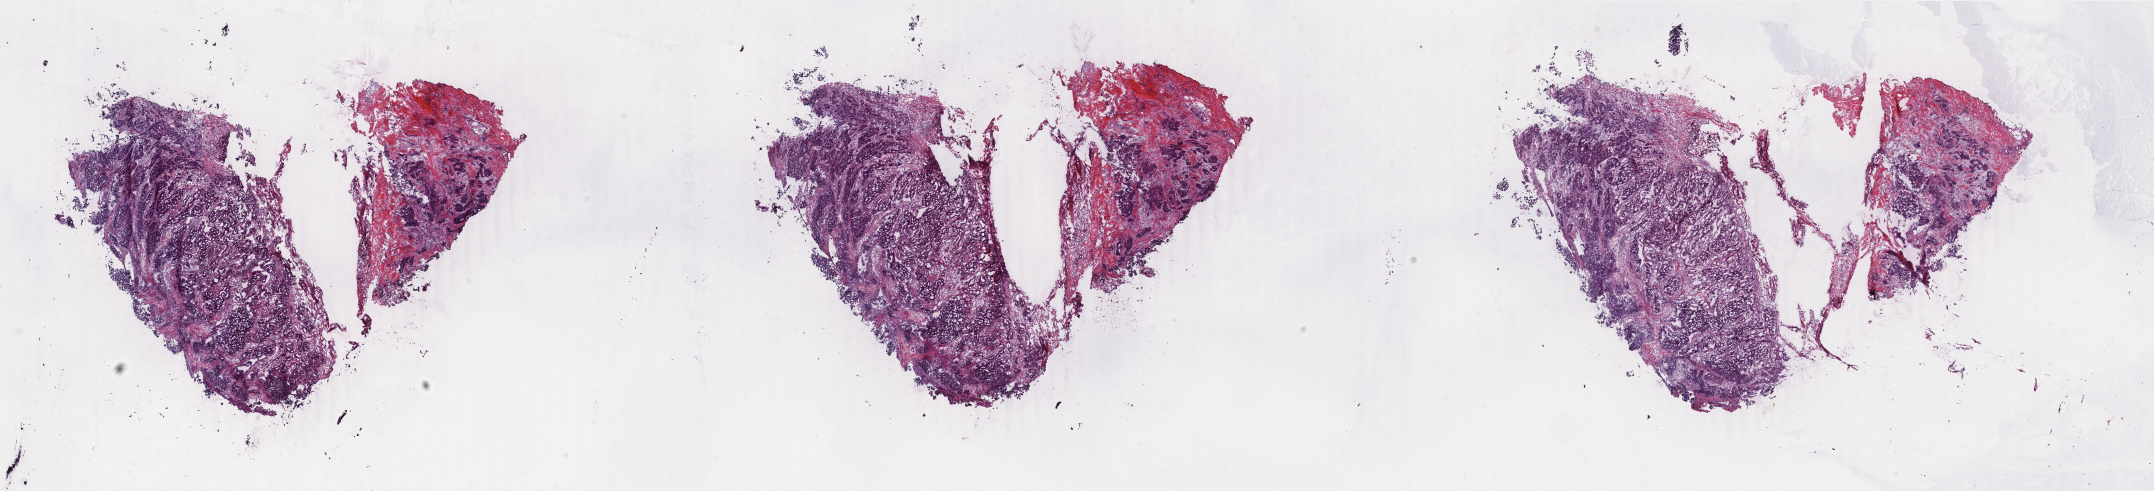
Digitized Hematoxylin and eosin (H&E) stained tissue section (whole slide) — low-resolution overview of the scanned area, about 34.3 x 7.8 mm (slide scanned at 40x); frozen section from the top of the tissue portion; sample: primary tumour, breast. Female patient; age at initial diagnosis 75 years. Composition of this section per pathologist review: tumour cells 80%, tumour nuclei 80%, normal cells 2%, stromal cells 18%, necrosis 0%. Inflammatory infiltration, as recorded: lymphocyte infiltration 1%, monocyte infiltration 0%, neutrophil infiltration 0%.
* AJCC pathologic stage: IIB (4th edition)
* pathologic diagnosis: Infiltrating duct mixed with other types of carcinoma
* laterality: right
* TNM: T3 N0 (i-) M0